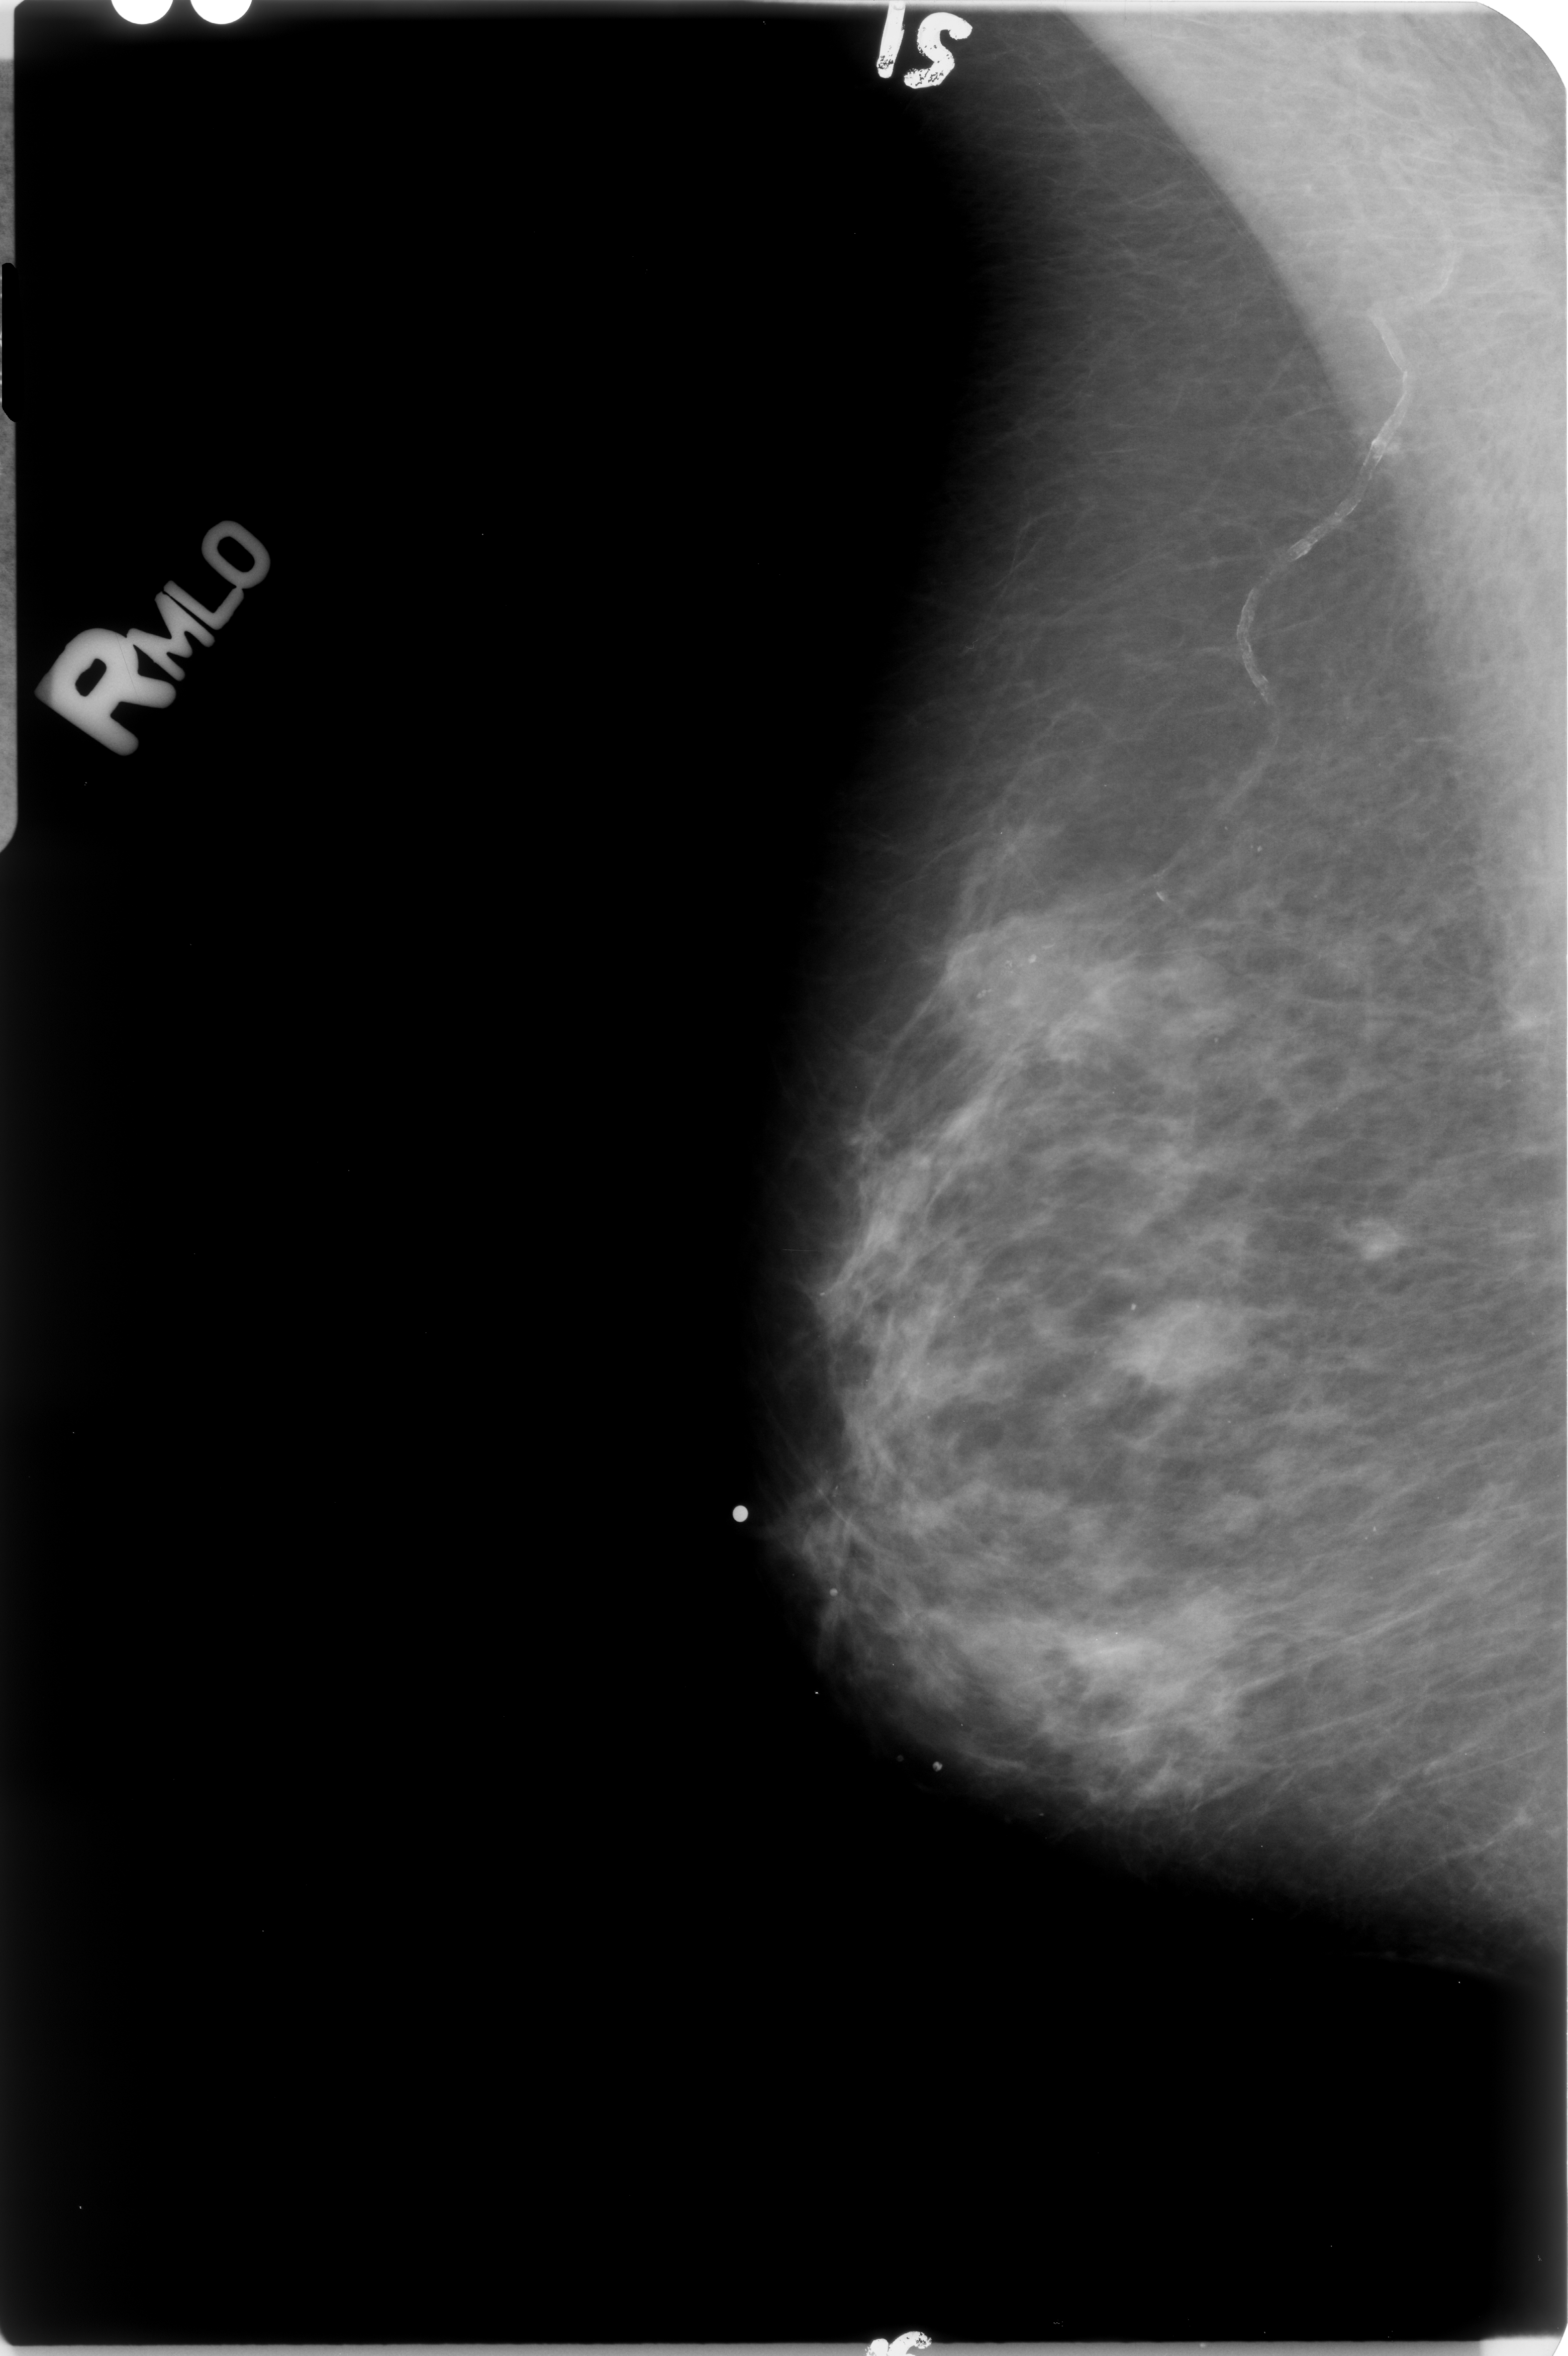
Digitized screen-film mammogram. Right breast. Mediolateral oblique (MLO) view. Breast composition: scattered fibroglandular densities (BI-RADS density category 2 of 4). 1568 × 2356 image matrix.
Marked abnormalities (boxes around the expert regions of interest):
- mass; BI-RADS assessment category 0; pathology (as recorded): benign: bounding box [x1, y1, x2, y2] px = [1115, 1300, 1237, 1393]